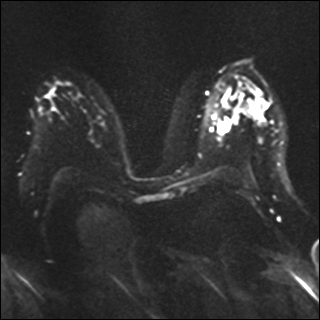
Breast MRI, one axial slice; slice 21 of 41 in the series (ordered by position); diffusion-weighted series; image 2 of 4 stored at this slice position (different b-values; order by instance number); 1.5 T; 320 × 320 image matrix. Female patient.
Annotated regions visible in this slice (manually delineated by an expert):
- tumour on diffusion-weighted imaging: box from (x=217, y=117) to (x=231, y=134) px